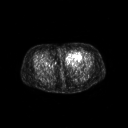
FDG PET of an extremity soft-tissue mass (from a PET/CT study), one axial slice. Slice 32 of 267 in the series (ordered by position). 128 × 128 image matrix. Female patient, age 47 years. Case-level facts recorded for this patient, not image findings: histological type: myxofibrosarcoma; grade: intermediate; site of the primary tumour: left thigh.
Outlined on this slice (expert contour drawn on MRI and transferred to this co-registered scan by the dataset authors):
- gross tumour volume including surrounding oedema: bounding box [x1, y1, x2, y2] px = [65, 51, 83, 66]
- gross tumour volume (mass): [66, 51, 82, 63]